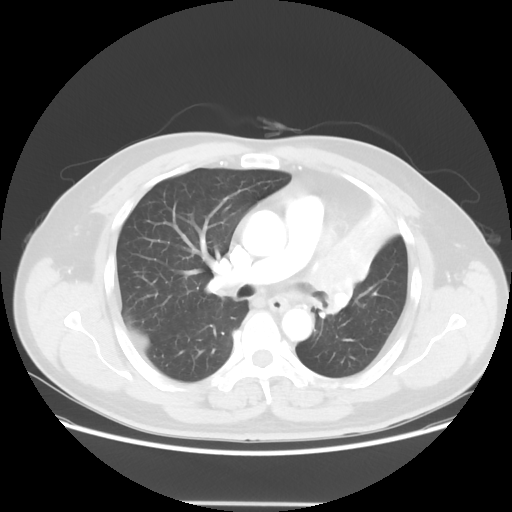
Chest CT, one axial slice; slice 38 of 62 in the series (ordered by position); reconstruction kernel STANDARD; lung window (W 1500 / L -600 HU); 5 mm slice thickness; 512 × 512 image matrix, field of view 403 × 403 mm. Male patient, age 49 years. From the clinical record (not read from this slice): clinical TNM (as recorded): T3 N3 M1c.
Structures marked on this image (rectangle marked by the reading radiologist):
- lung tumour (recorded histology: squamous cell carcinoma): bounding box <304,228,373,323> (left, top, right, bottom; pixels)